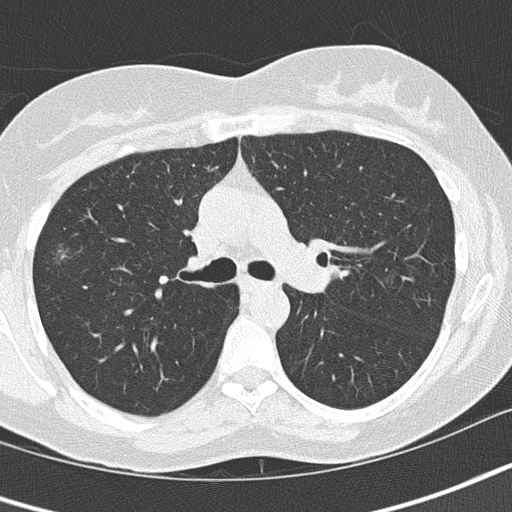
Axial slice from a low-dose chest CT screening exam, baseline screening round, lung window (W 1500 / L -600 HU), 512 × 512 image matrix, field of view 280 × 280 mm. Female participant, aged 64 years at enrolment. Former smoker at enrolment.
Lesion marked by an expert reader, bounding box (x1, y1, x2, y2) in pixels: (25, 227, 86, 287). The screening reader recorded 4 non-calcified nodules or masses ≥4 mm on this exam (right upper lobe, left upper lobe, left upper lobe, left lower lobe); which of them this box marks is not recorded. Lung cancer was diagnosed 447 days after this screen: bronchiolo-alveolar adenocarcinoma, NOS, right upper lobe, well differentiated (G1), stage IA (AJCC 6th edition), 10 mm at pathology.